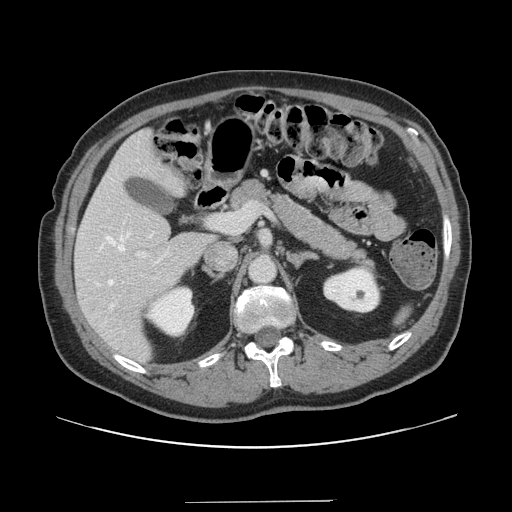
Contrast-enhanced abdominal CT, one axial slice; slice 83 of 151 in the series (ordered by position); 120 kVp; intravenous contrast given; soft-tissue window (W 400 / L 40 HU); 2.5 mm slice thickness; 512 × 512 image matrix, field of view 399 × 399 mm. Male patient, age 63 years. From the clinical record (not read from this slice): diagnosis: colorectal cancer liver metastases, imaged before liver resection; multiple liver metastases: no; largest metastasis: 2.1 cm.
Outlined on this slice (outlined manually by an expert reader):
- hepatic veins: box from (x=106, y=234) to (x=129, y=306) px
- liver: (x=76, y=131)–(x=214, y=362)
- planned liver remnant (the part of the liver to remain after resection): (x=76, y=131)–(x=213, y=362)
- portal vein (with intrahepatic branches): (x=136, y=203)–(x=254, y=258)